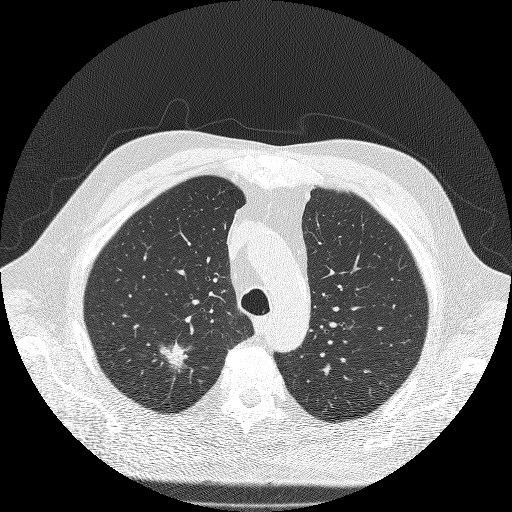
Low-dose screening chest CT, one axial slice; position 146 of 180 along the scan axis; reconstruction kernel FC51; 120 kVp; lung window (W 1500 / L -600 HU); 2 mm slice thickness; 512 × 512 image matrix, field of view 385 × 385 mm.
Annotated regions visible in this slice (expert manual segmentation):
- lesion 1 (tumor, upper lobe of right lung): bounding box <160,341,188,369> (left, top, right, bottom; pixels)